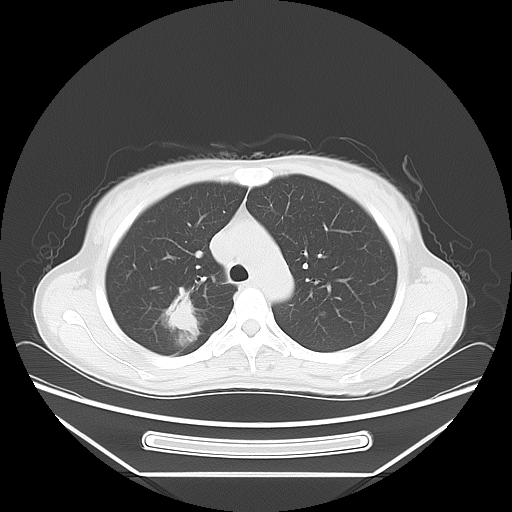
Chest CT, one axial slice. Position 48 of 66 along the scan axis. Reconstruction kernel LUNG. 120 kVp. Lung window (W 1500 / L -600 HU). 5 mm slice thickness. 512 × 512 image matrix. Patient: female, 37 years. From the clinical record (not read from this slice): clinical TNM (as recorded): T1c N0 M1.
Annotated regions visible in this slice (bounding box drawn by a radiologist):
- lung tumour (recorded histology: adenocarcinoma): bounding box <163,283,204,345> (left, top, right, bottom; pixels)